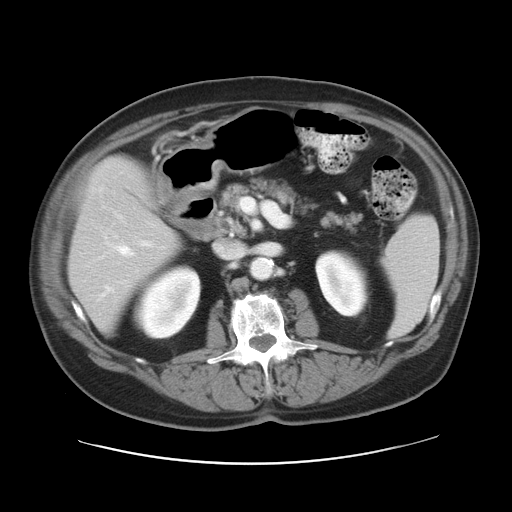
Contrast-enhanced abdominal CT, one axial slice; position 14 of 28 along the scan axis; reconstruction kernel STANDARD; 120 kVp; intravenous contrast given; soft-tissue window (W 400 / L 40 HU); 7.5 mm slice thickness; 512 × 512 image matrix, field of view 402 × 402 mm. Male patient, age 74 years. From the clinical record (not read from this slice): diagnosis: colorectal cancer liver metastases, imaged before liver resection; multiple liver metastases: no; largest metastasis: 5 cm; disease in both lobes: no.
Outlined on this slice (manually delineated by an expert):
- hepatic veins: box from (x=105, y=241) to (x=153, y=292) px
- liver: (x=68, y=159)–(x=176, y=330)
- planned liver remnant (the part of the liver to remain after resection): (x=68, y=166)–(x=176, y=330)